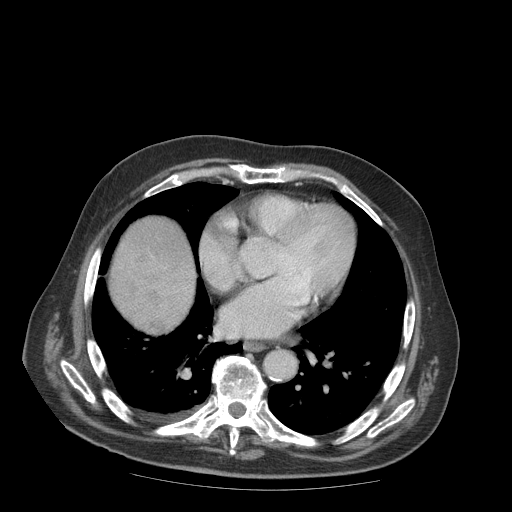
Contrast-enhanced abdominal CT (liver protocol), one axial slice. Position 92 of 99 along the scan axis. Reconstruction kernel STANDARD. 140 kVp. Soft-tissue window (W 400 / L 40 HU). 2.5 mm slice thickness. 512 × 512 image matrix. Case-level facts recorded for this patient, not image findings: diagnosis: hepatocellular carcinoma (patient treated with transarterial chemoembolisation; whether this scan precedes or follows treatment is not stated here); TNM stage (as recorded): Stage-IIIB; Child-Pugh class: A; tumour nodularity: multinodular.
Structures marked on this image (semi-automatically segmented with operator editing):
- abdominal aorta: box from (x=265, y=349) to (x=295, y=378) px
- liver parenchyma outside the tumour (the mass and vessels are separate outlines, so this box may not span the whole liver): (x=110, y=216)–(x=196, y=328)